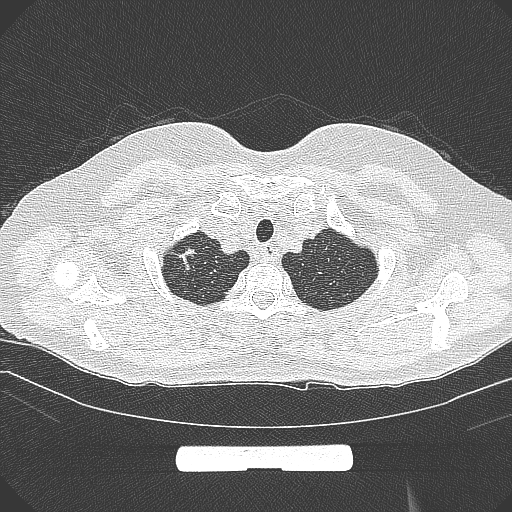
Chest CT, one axial slice. Position 265 of 295 along the scan axis. 120 kVp. Lung window (W 1500 / L -600 HU). 1 mm slice thickness. 512 × 512 image matrix, field of view 369 × 369 mm. Patient: female, 58 years. Case-level facts recorded for this patient, not image findings: clinical TNM (as recorded): T1b N0 M0; histopathological grade: G2-3.
Annotated regions visible in this slice (rectangle marked by the reading radiologist):
- lung tumour (recorded histology: adenocarcinoma): bounding box [x1, y1, x2, y2] px = [172, 243, 198, 280]